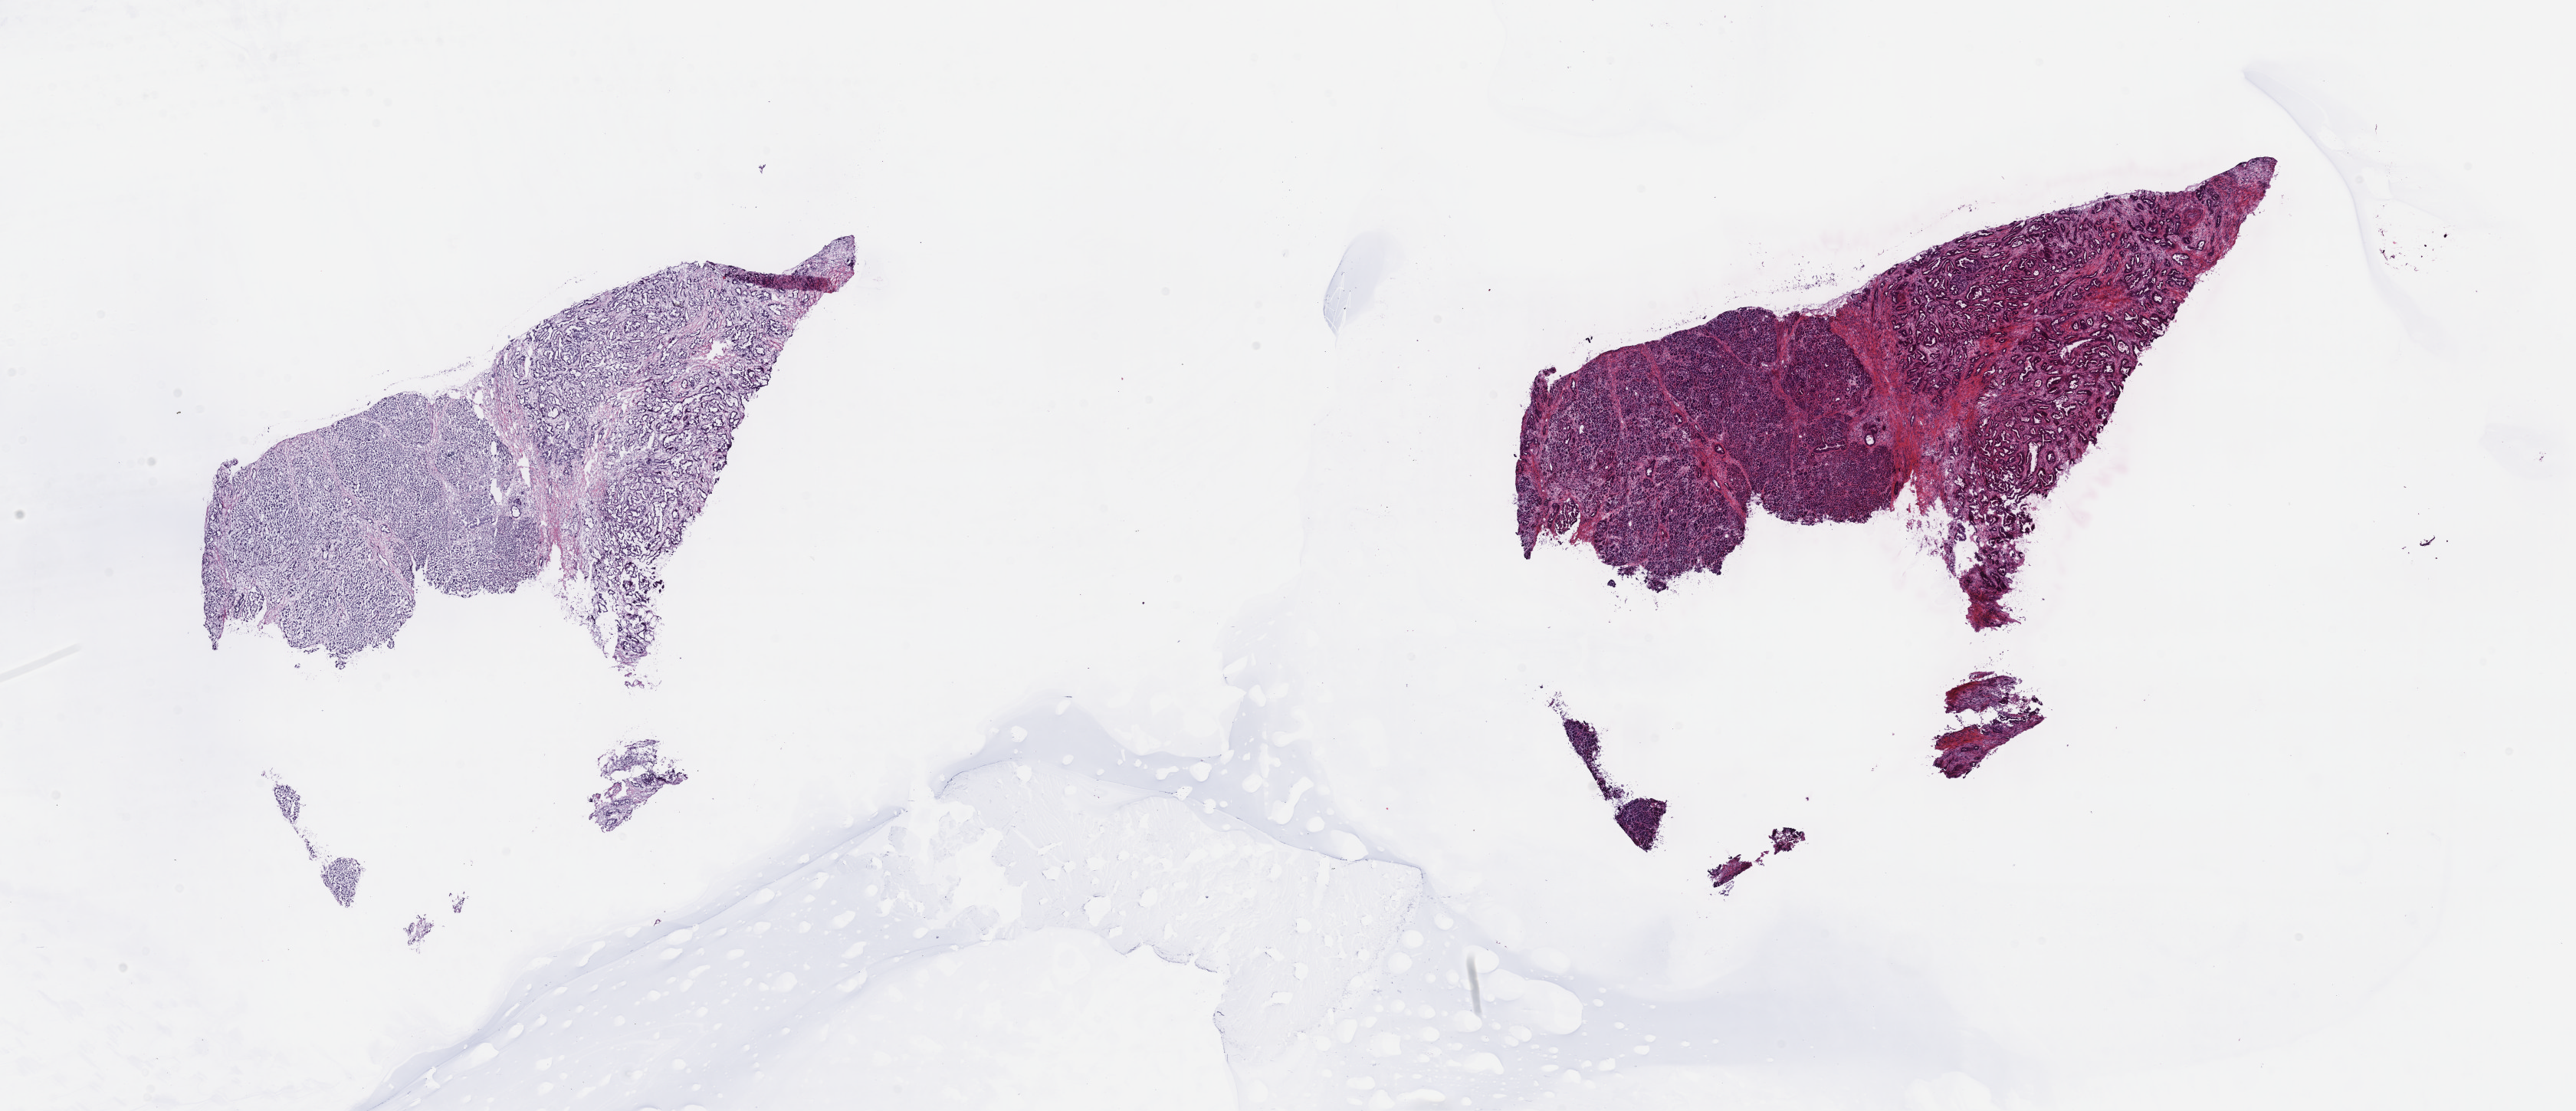
Whole-slide histology image, H&E-stained, whole scanned area (about 27.2 x 11.7 mm, from a 40x scan) shown as a low-resolution overview, frozen section from the top of the tissue portion, sample: primary tumour, pancreas. Patient: female, age at initial diagnosis 64 years. Histologic grade: G1 (well differentiated). Composition of this section per pathologist review: tumour cells 80%, tumour nuclei 80%, normal cells 0%, stromal cells 20%, necrosis 0%. Infiltration values recorded for this section: lymphocyte infiltration 40%, monocyte infiltration 20%, neutrophil infiltration 20%.
- diagnosis: Infiltrating duct carcinoma, NOS (head of pancreas)
- AJCC pathologic stage: IIA (7th edition)